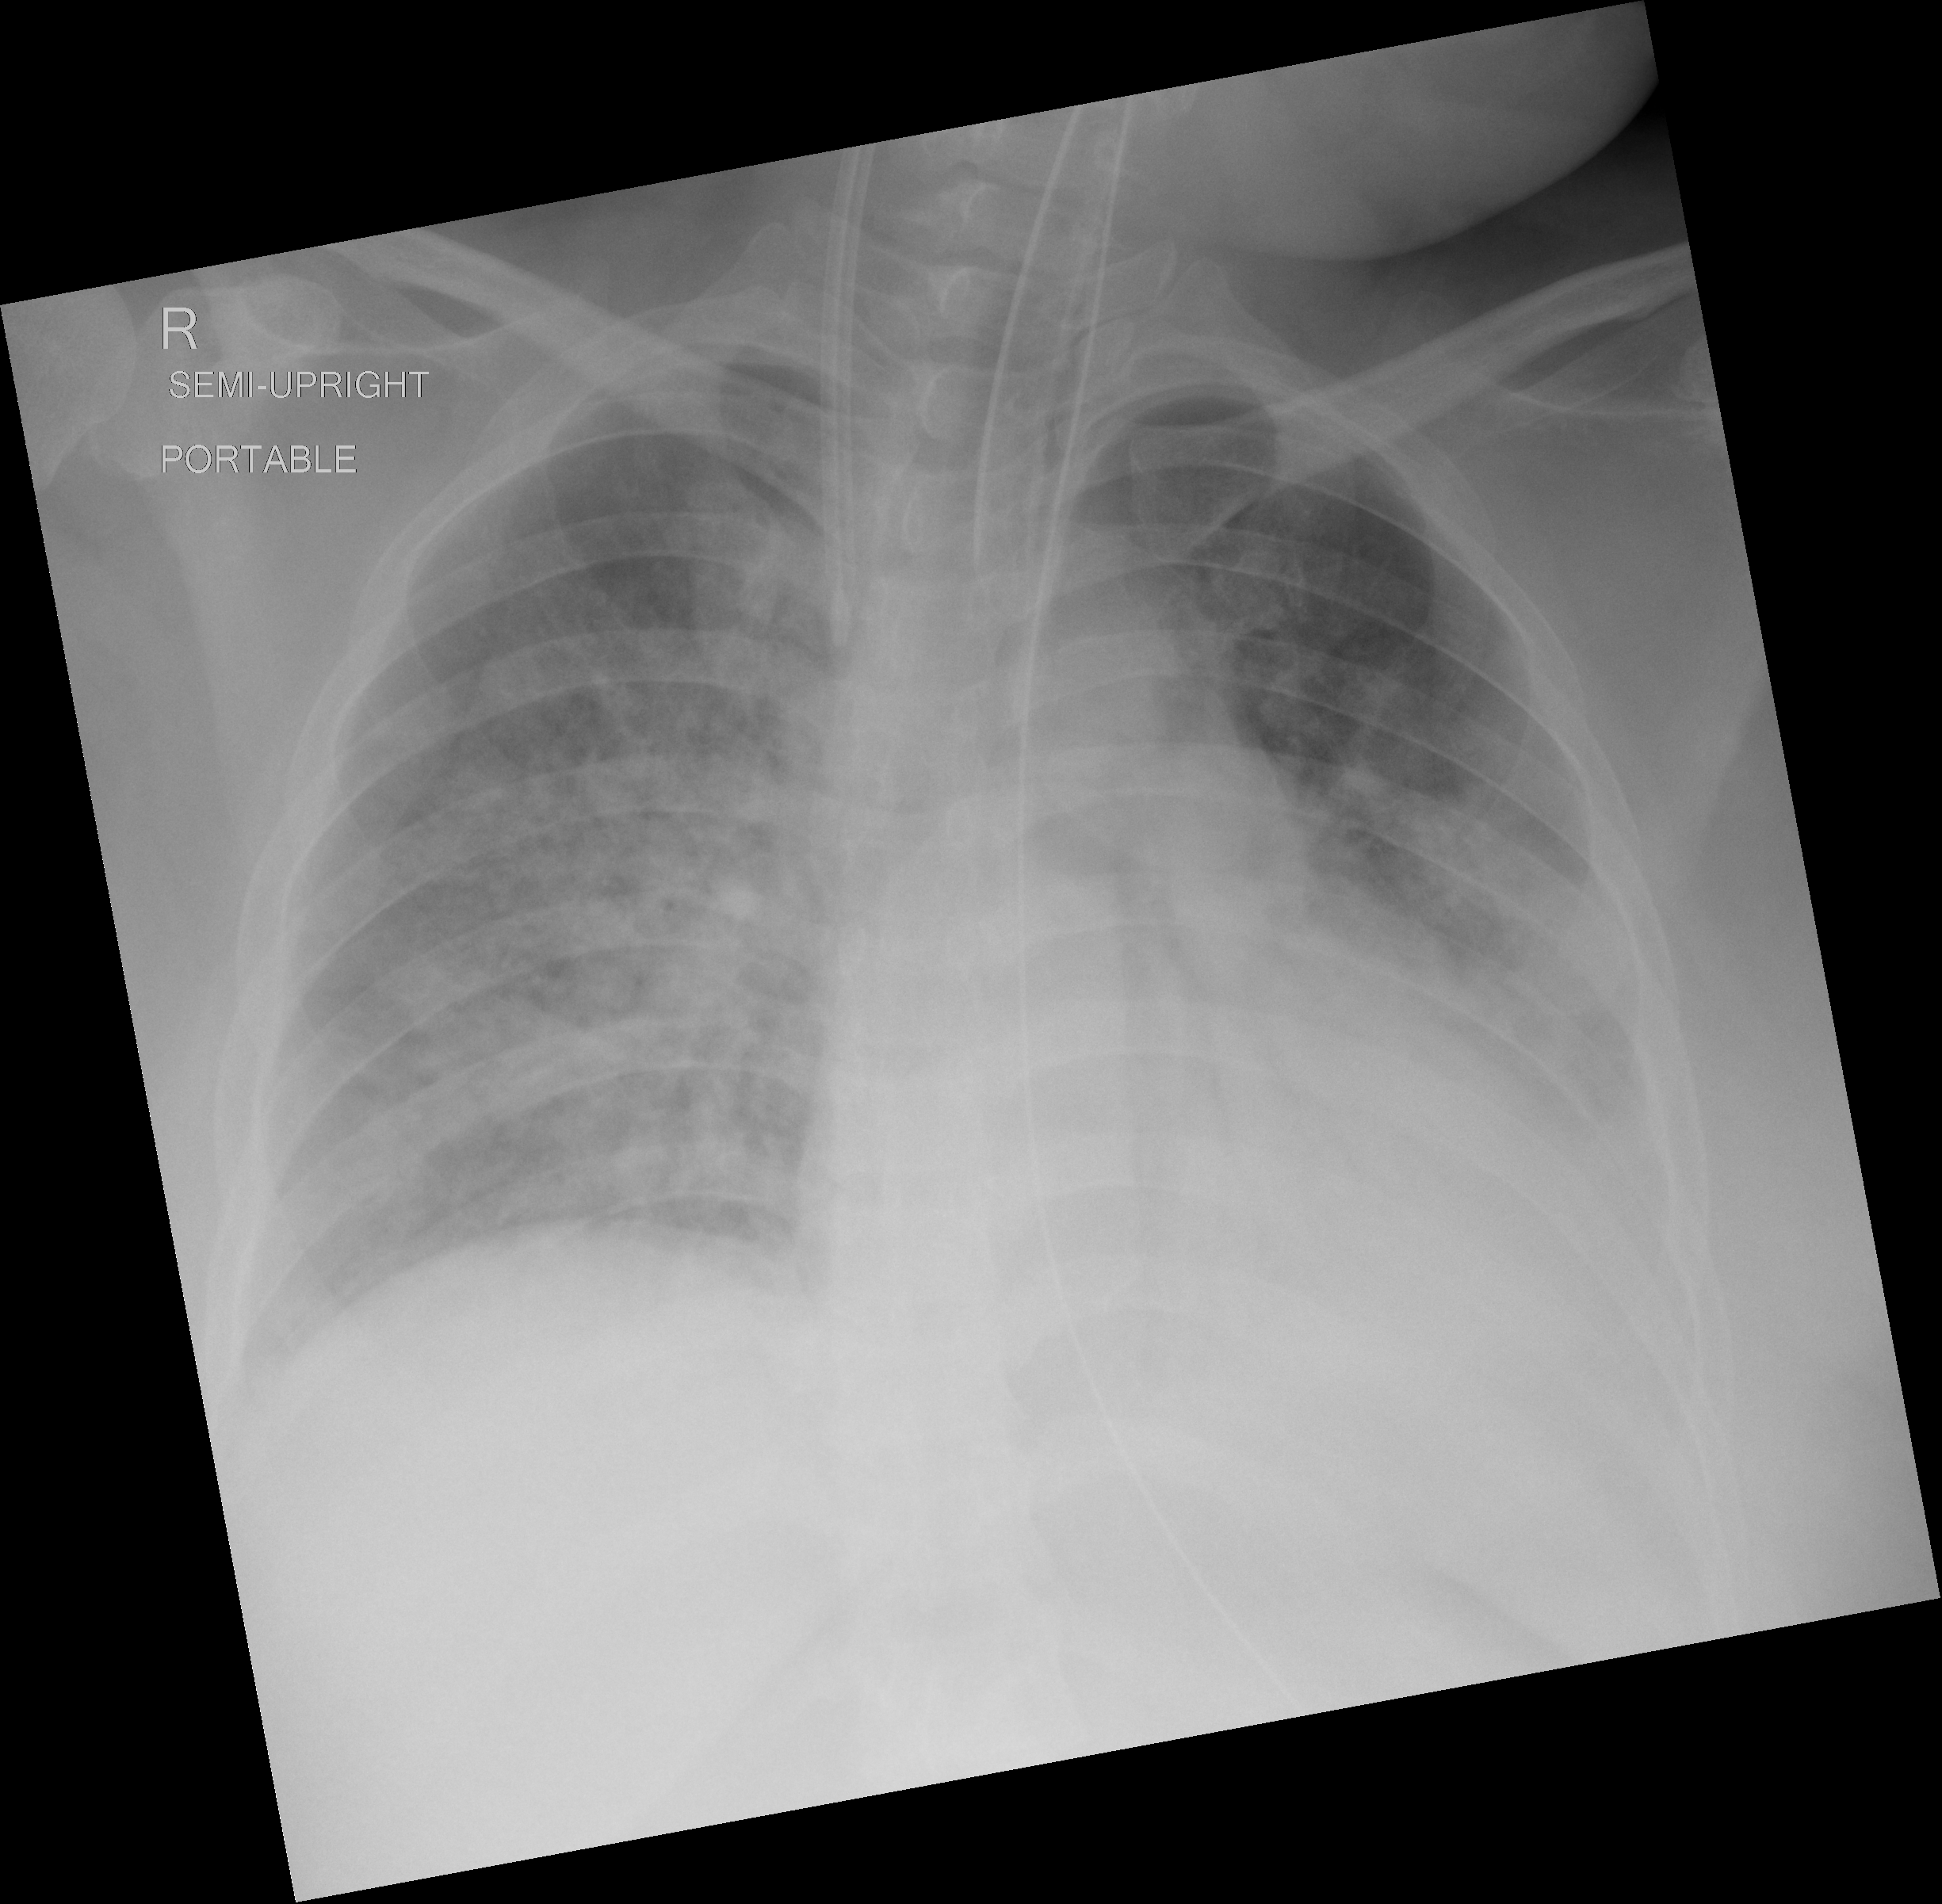
Chest X-ray (portable), AP projection. Female patient, age 37 years; imaged 2 days after the COVID-19 diagnosis.
Radiologist's key findings for this exam: Worsening bilateral airspace disease predominately in the perihilar regions and in the mid left lung.